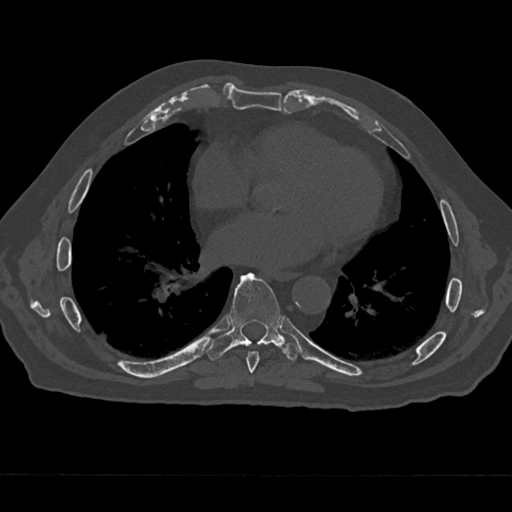
CT including the spine, one axial slice. Slice 336 of 797 in the series (ordered by position). Reconstruction kernel Br40s/3. 120 kVp. Bone window (W 1800 / L 400 HU). 512 × 512 image matrix, field of view 377 × 377 mm. Male patient, age 75 years. Case-level facts recorded for this patient, not image findings: primary cancer: renal.
Annotated regions visible in this slice (semi-automatic segmentation, software-assisted and operator-edited):
- T7 vertebra: bounding box <246,351,260,377> (left, top, right, bottom; pixels)
- T8 vertebra: <207,272,300,361>